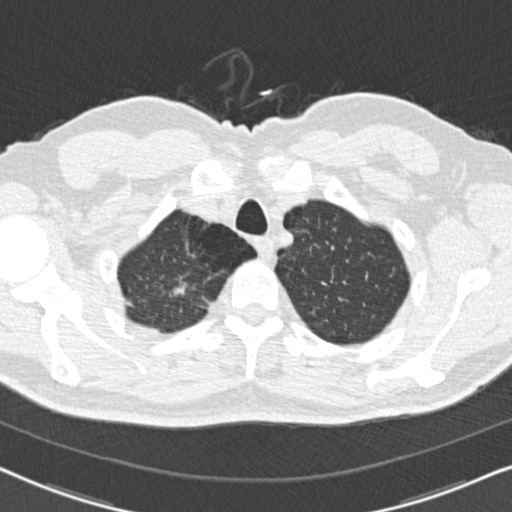
Chest CT (low-dose screening protocol), one axial image; baseline annual screen; lung window (W 1500 / L -600 HU); 2 mm slice thickness. Male, age 56 years at enrolment. Former smoker at enrolment.
Expert reader's lesion annotation, box from (x=150, y=270) to (x=202, y=313) px. No non-calcified nodule or mass ≥4 mm was recorded by the screening reader at this exam. Official screen result: negative screen, minor abnormalities not suspicious for lung cancer. Later outcome: lung cancer diagnosed 756 days after this screen — adenocarcinoma, NOS, right upper lobe, moderately differentiated (G2), stage IA (AJCC 6th edition), 9 mm at pathology.